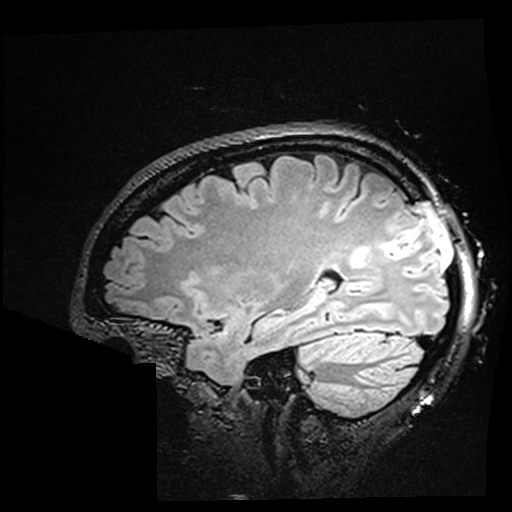
Brain MRI from a brain-tumour surgery series, one sagittal slice. Position 120 of 176 along the scan axis. T2 FLAIR. 1 mm slice thickness. 512 × 512 image matrix, field of view 250 × 250 mm. Case-level facts recorded for this patient, not image findings: histopathology: Oligodendroglioma; WHO grade: 2.
Structures marked on this image (manually delineated by an expert):
- residual tumour: bounding box <350,246,370,267> (left, top, right, bottom; pixels)